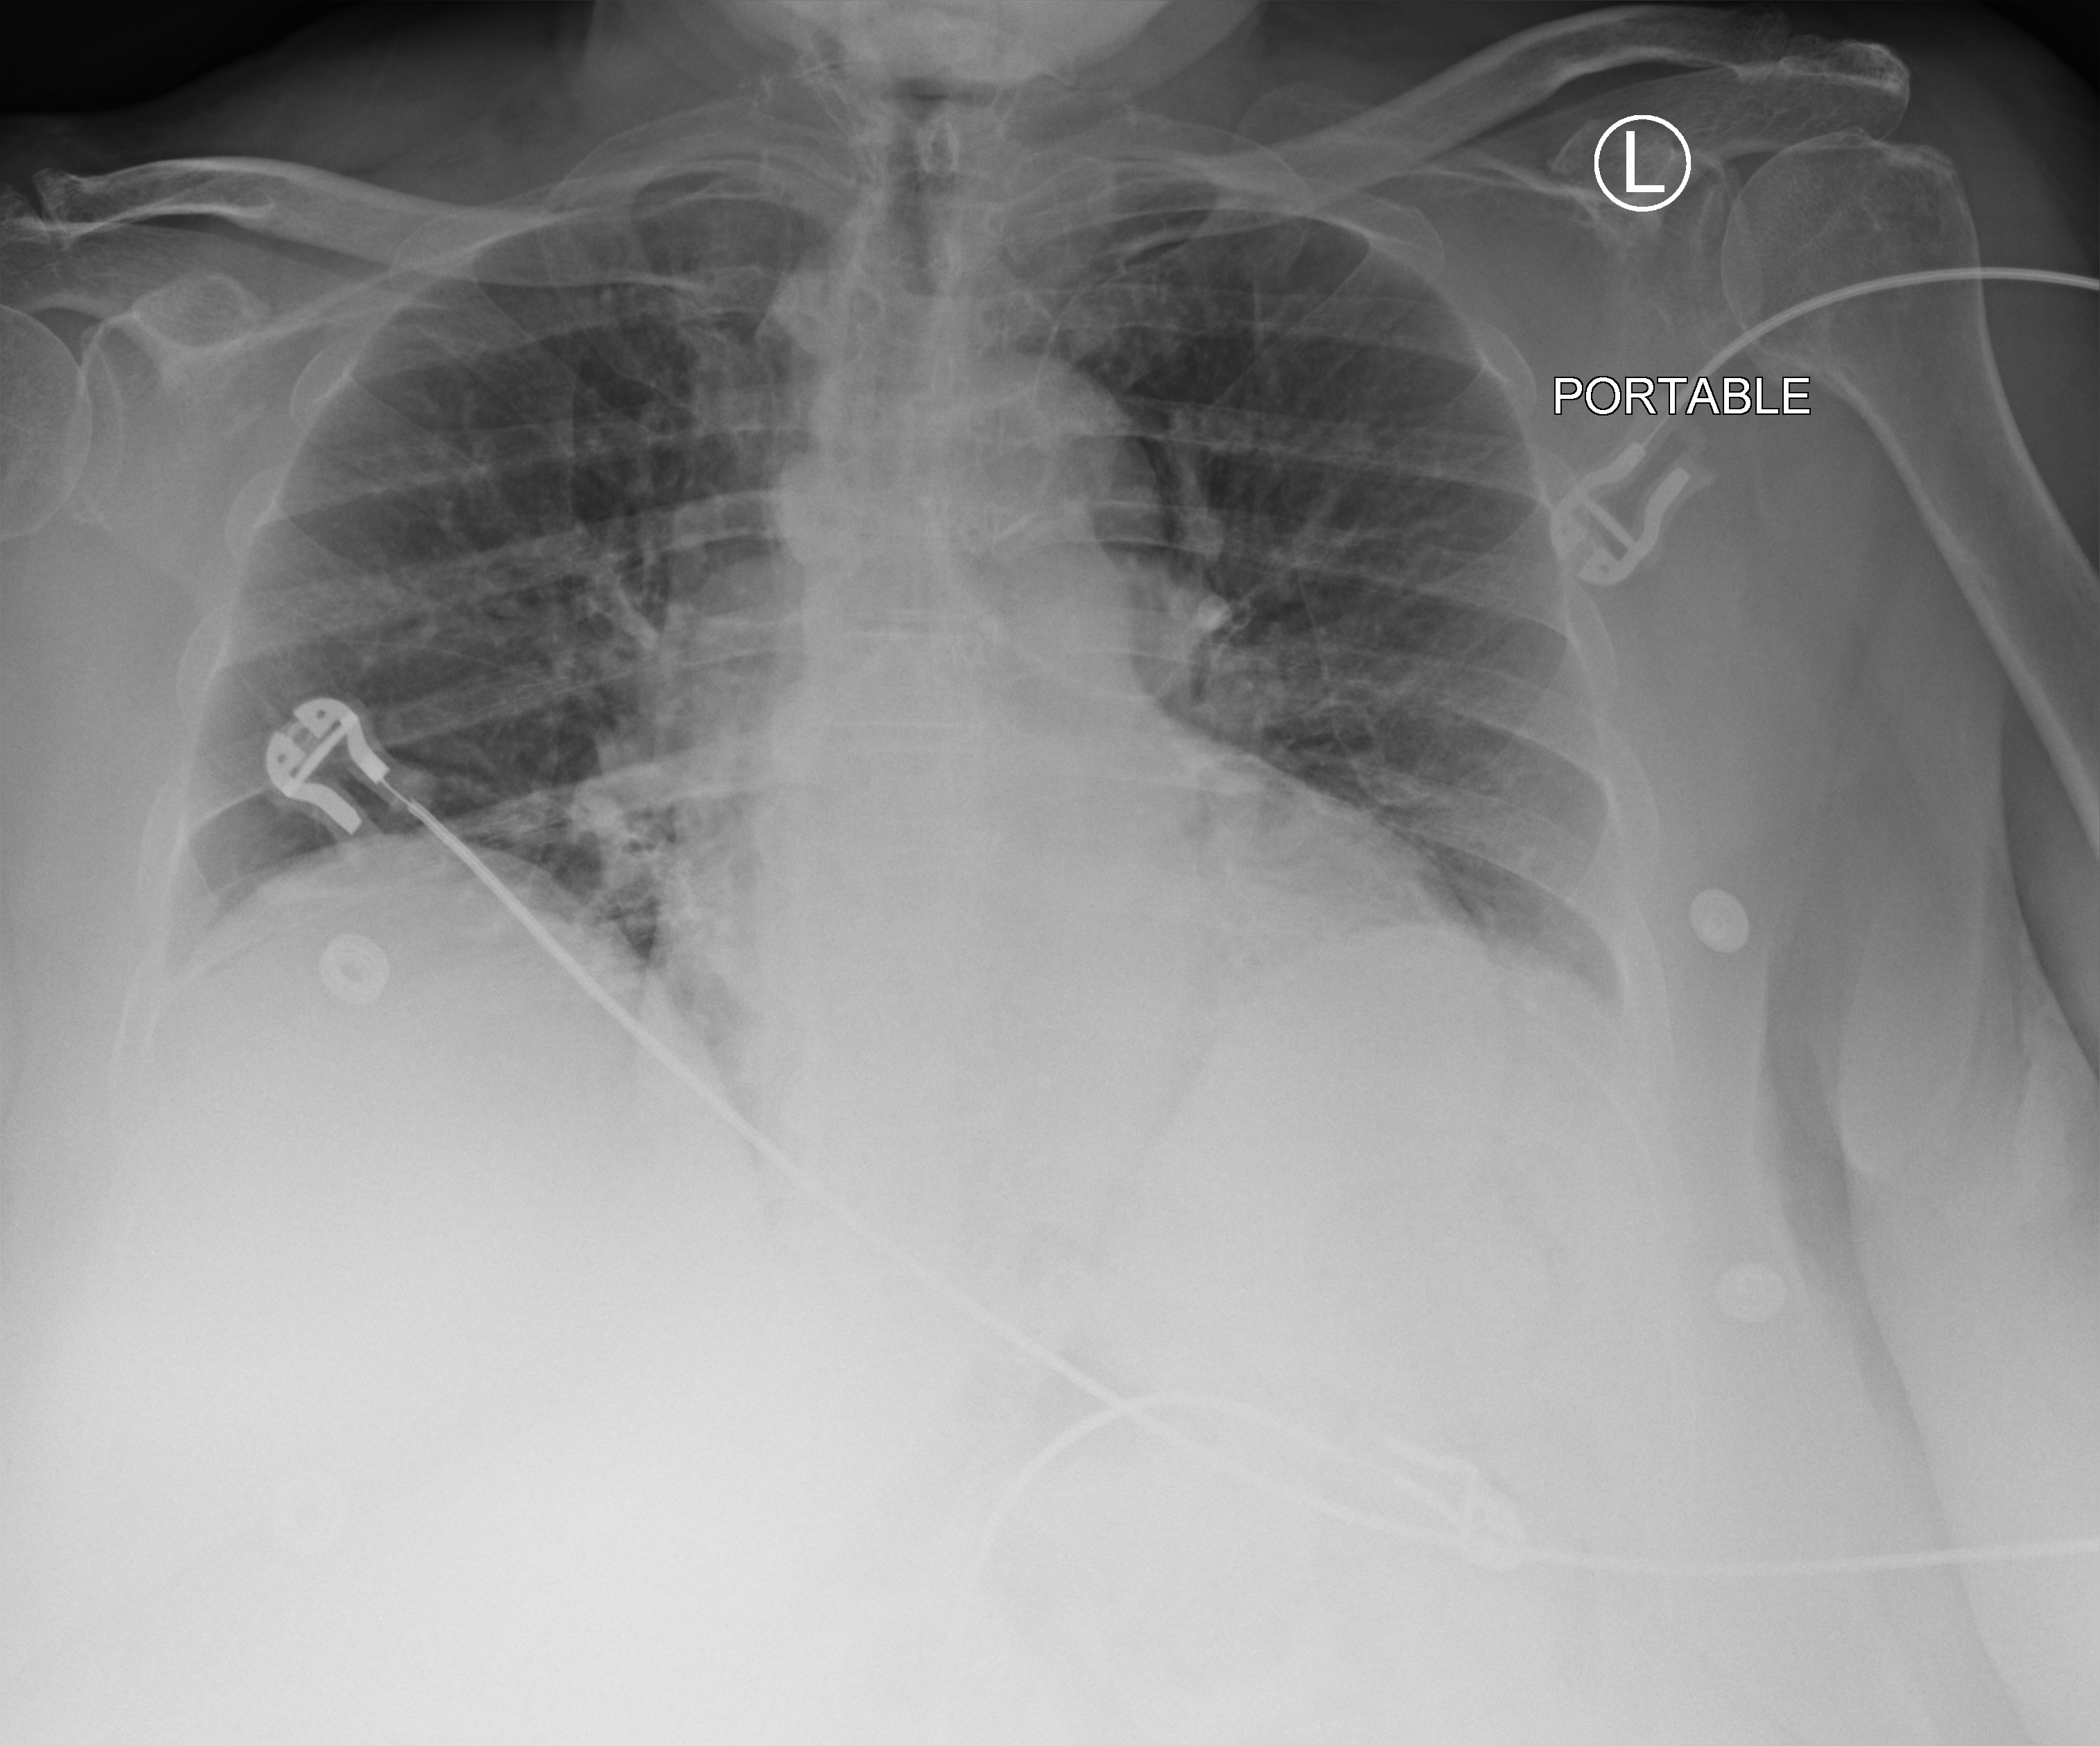
Portable chest radiograph, anteroposterior (AP) projection. Female patient hospitalised with COVID-19, age 75–90 years.
Admission-level facts for this patient (not findings on this image; timing relative to this image not recorded): admitted to intensive care during this hospital stay: no; chronic kidney disease (admission record): no; smoking status (admission record): never.